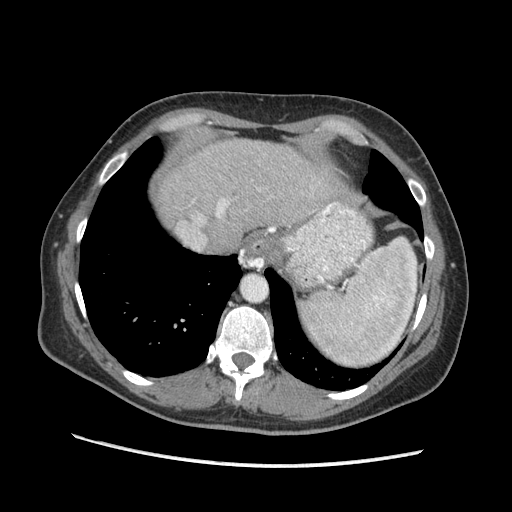
Contrast-enhanced abdominal CT (liver protocol), one axial slice; position 152 of 170 along the scan axis; soft-tissue window (W 400 / L 40 HU); 2.5 mm slice thickness; 512 × 512 image matrix. Case-level facts recorded for this patient, not image findings: diagnosis: hepatocellular carcinoma (patient treated with transarterial chemoembolisation; whether this scan precedes or follows treatment is not stated here); TNM stage (as recorded): Stage-II; Child-Pugh class: A; tumour differentiation: no biopsy; tumour nodularity: multinodular.
Structures marked on this image (semi-automatic segmentation, software-assisted and operator-edited):
- abdominal aorta: bounding box <241,275,267,301> (left, top, right, bottom; pixels)
- liver parenchyma outside the tumour (the mass and vessels are separate outlines, so this box may not span the whole liver): <156,138,338,238>
- liver vessels: <199,199,227,221>